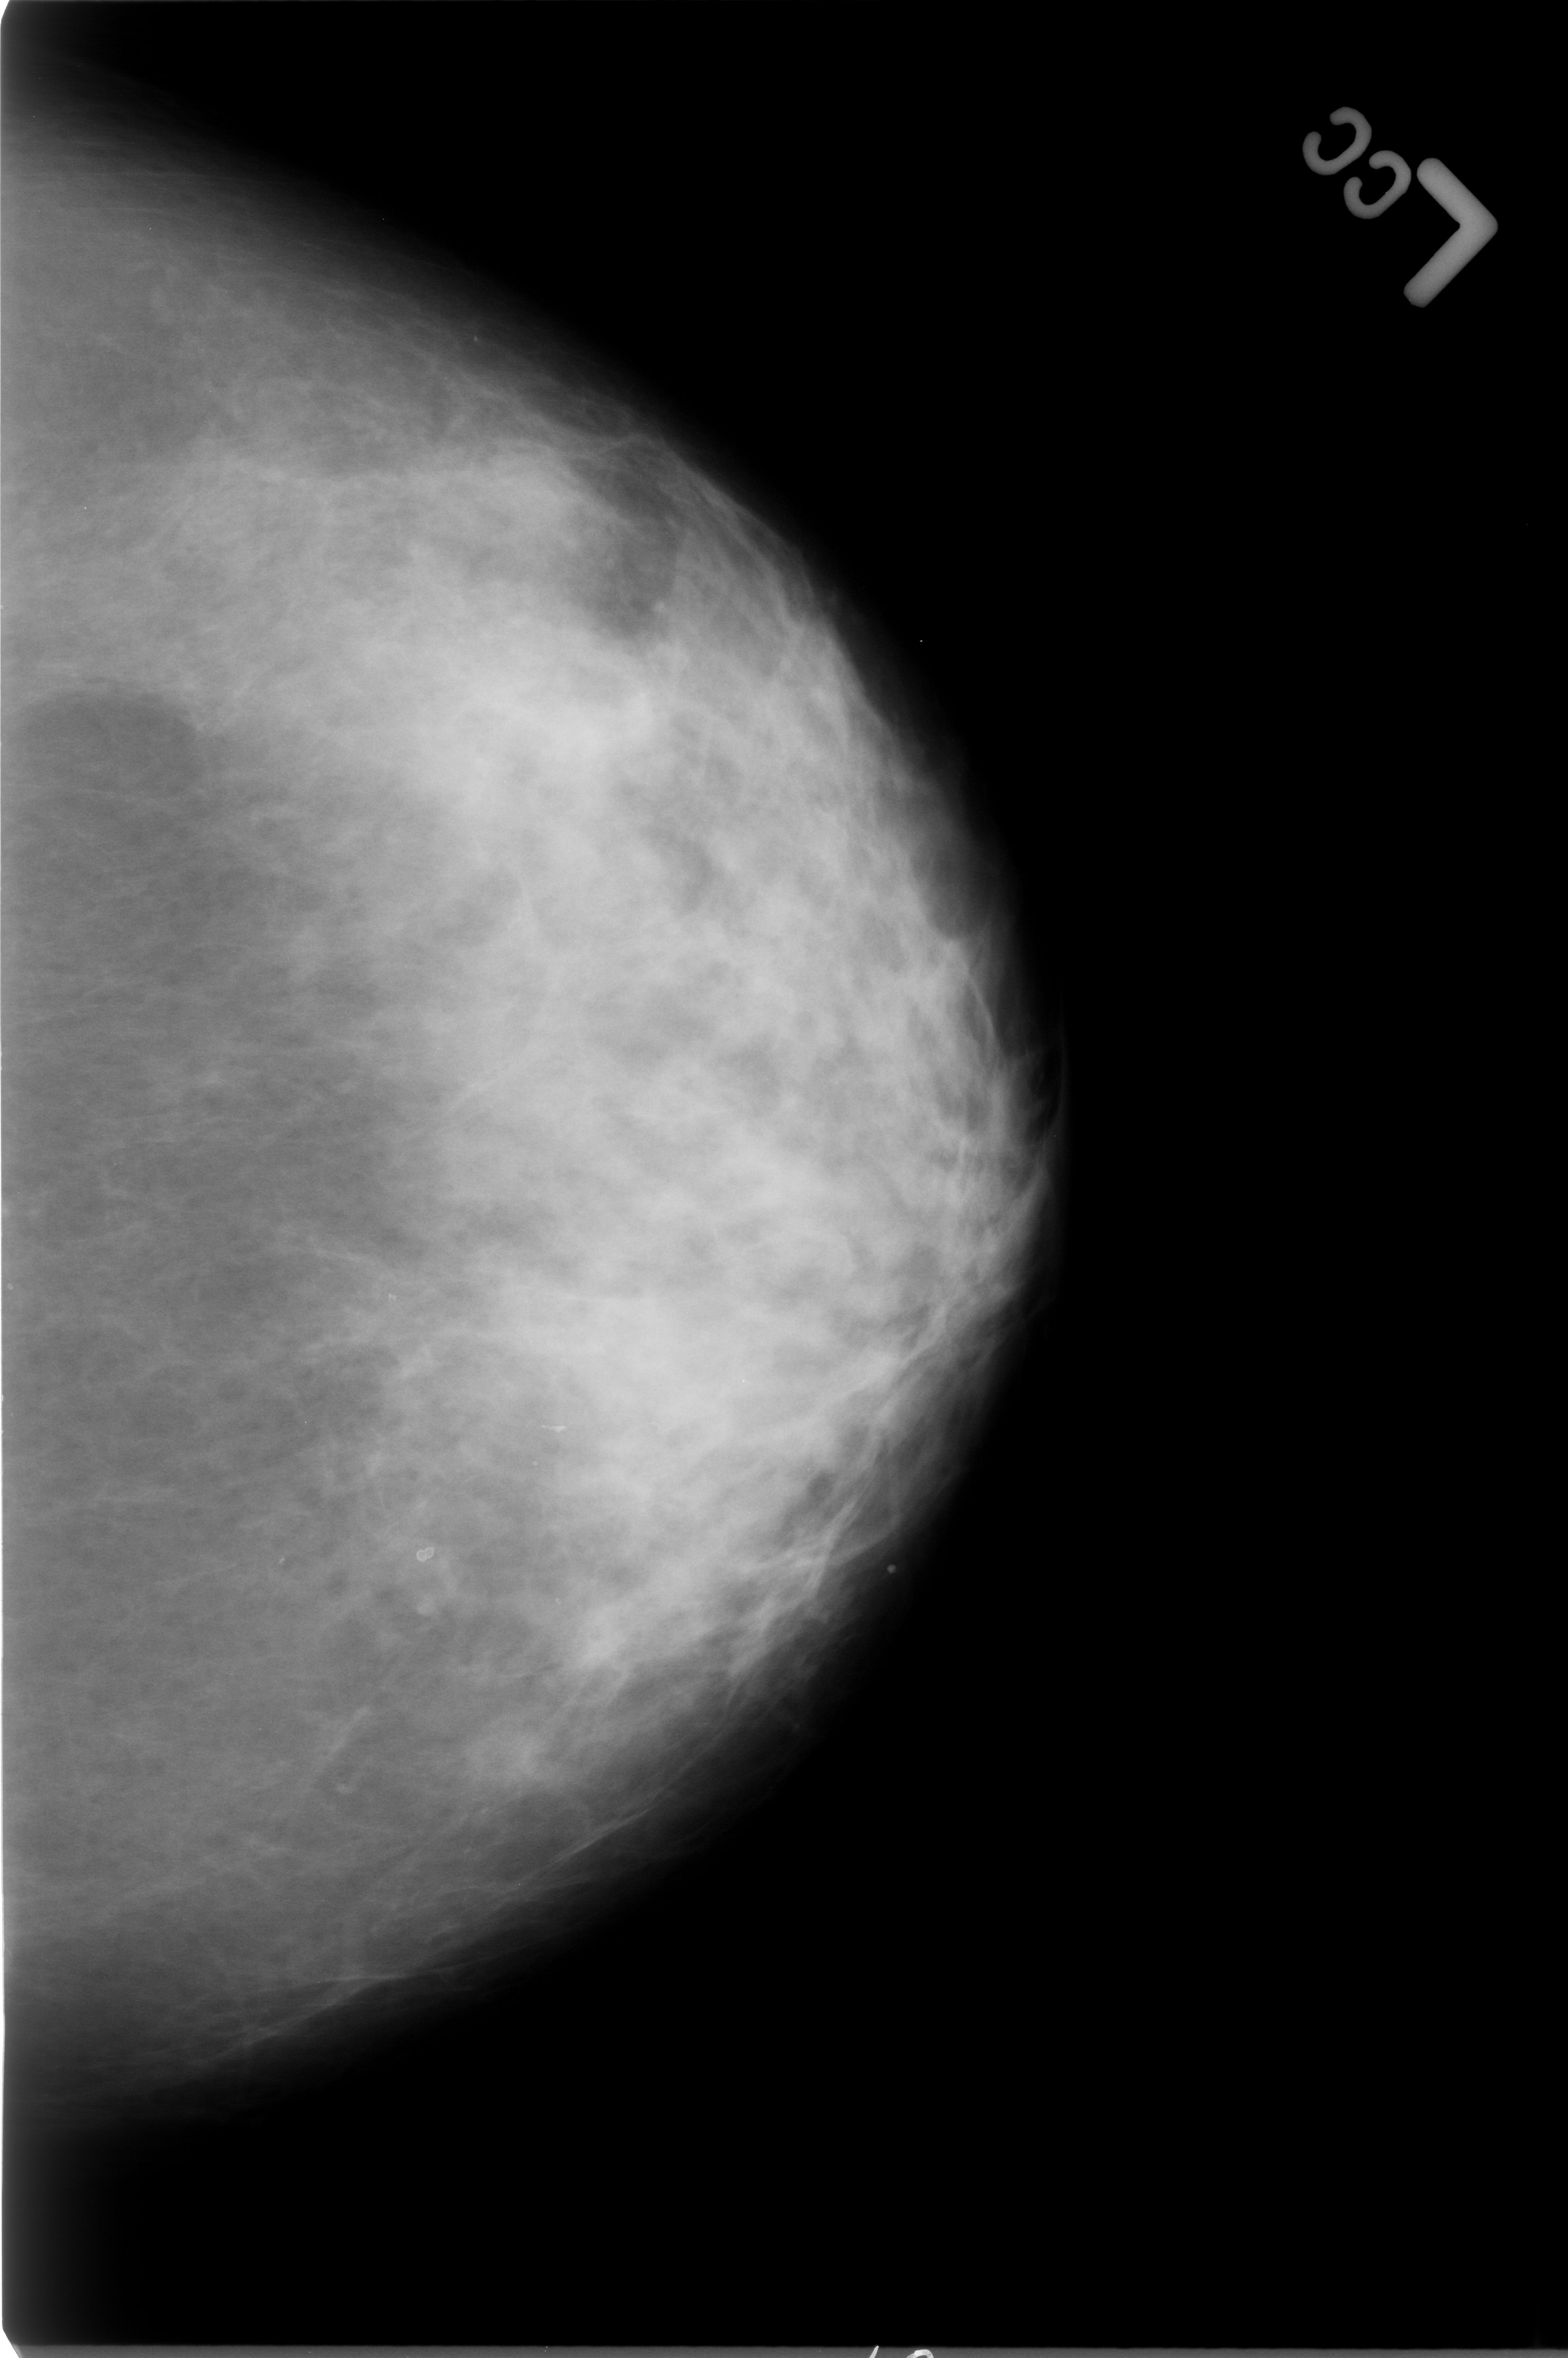
Scanned film-screen mammogram. Left breast. Craniocaudal (CC) view. BI-RADS breast density category 3 (scale 1–4). 1568 × 2358 image matrix.
Marked abnormalities (boxes around the expert regions of interest):
- Finding 1 of 2: calcifications, morphology round and regular / lucent centered; BI-RADS assessment category 2; outcome (as recorded, no biopsy): benign without callback (not worked up further): bounding box (x1, y1, x2, y2) in pixels: (399, 1534, 442, 1573)
- Finding 2 of 2: calcifications, morphology round and regular / lucent centered; BI-RADS assessment category 2; subtlety rating 3 on a 1 (subtle) to 5 (obvious) scale; outcome (as recorded, no biopsy): benign without callback (not worked up further): (536, 1405, 583, 1452)